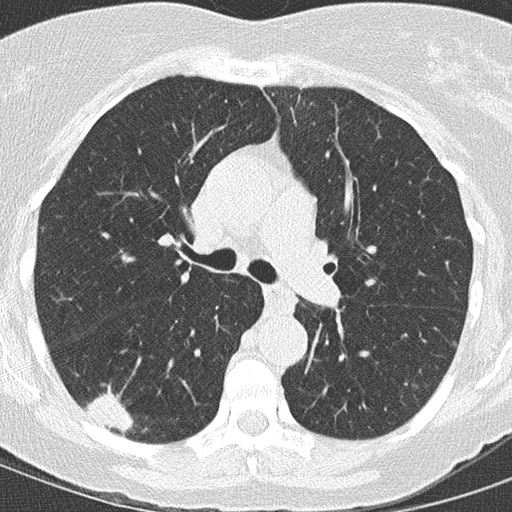
Axial slice from a low-dose chest CT screening exam; baseline annual screen; lung window (W 1500 / L -600 HU); 2 mm slice thickness. Female participant, aged 59 years at enrolment.
Lesion marked by an expert reader, bounding box [x1, y1, x2, y2] px = [71, 385, 147, 442]. The exam's reader record, not a measurement of the box and not confirmed to be the same lesion: non-calcified nodule or mass ≥4 mm, right lower lobe, 24 × 15 mm, spiculated (stellate) margins, soft tissue attenuation. Official screen result: positive, change unspecified: nodule(s) >= 4 mm or enlarging nodule(s), mass(es), or other non-specific abnormalities suspicious for lung cancer. Lung cancer was diagnosed 12 days after this screen: adenocarcinoma, NOS, right lower lobe, moderately differentiated (G2), stage IIB (AJCC 6th edition), 22 mm at pathology.